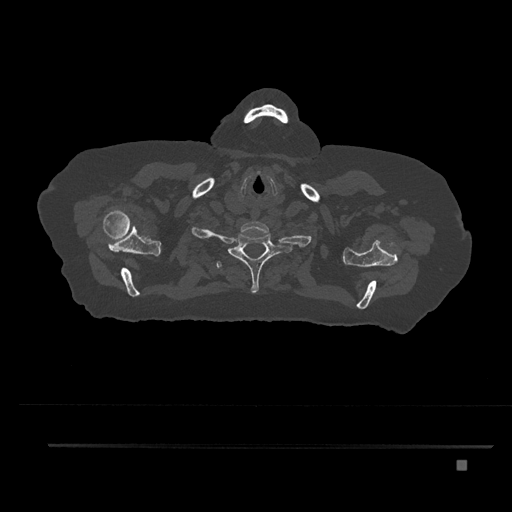
CT including the spine, one axial slice; 120 kVp; bone window (W 1800 / L 400 HU); 512 × 512 image matrix. Female patient, age 76 years. Case-level facts recorded for this patient, not image findings: primary cancer: lung; vertebrae with lytic lesions (as recorded): T11, L3.
Annotated regions visible in this slice (semi-automatic segmentation, software-assisted and operator-edited):
- T1 vertebra: bounding box <228,232,283,293> (left, top, right, bottom; pixels)
- T2 vertebra: <216,261,222,269>